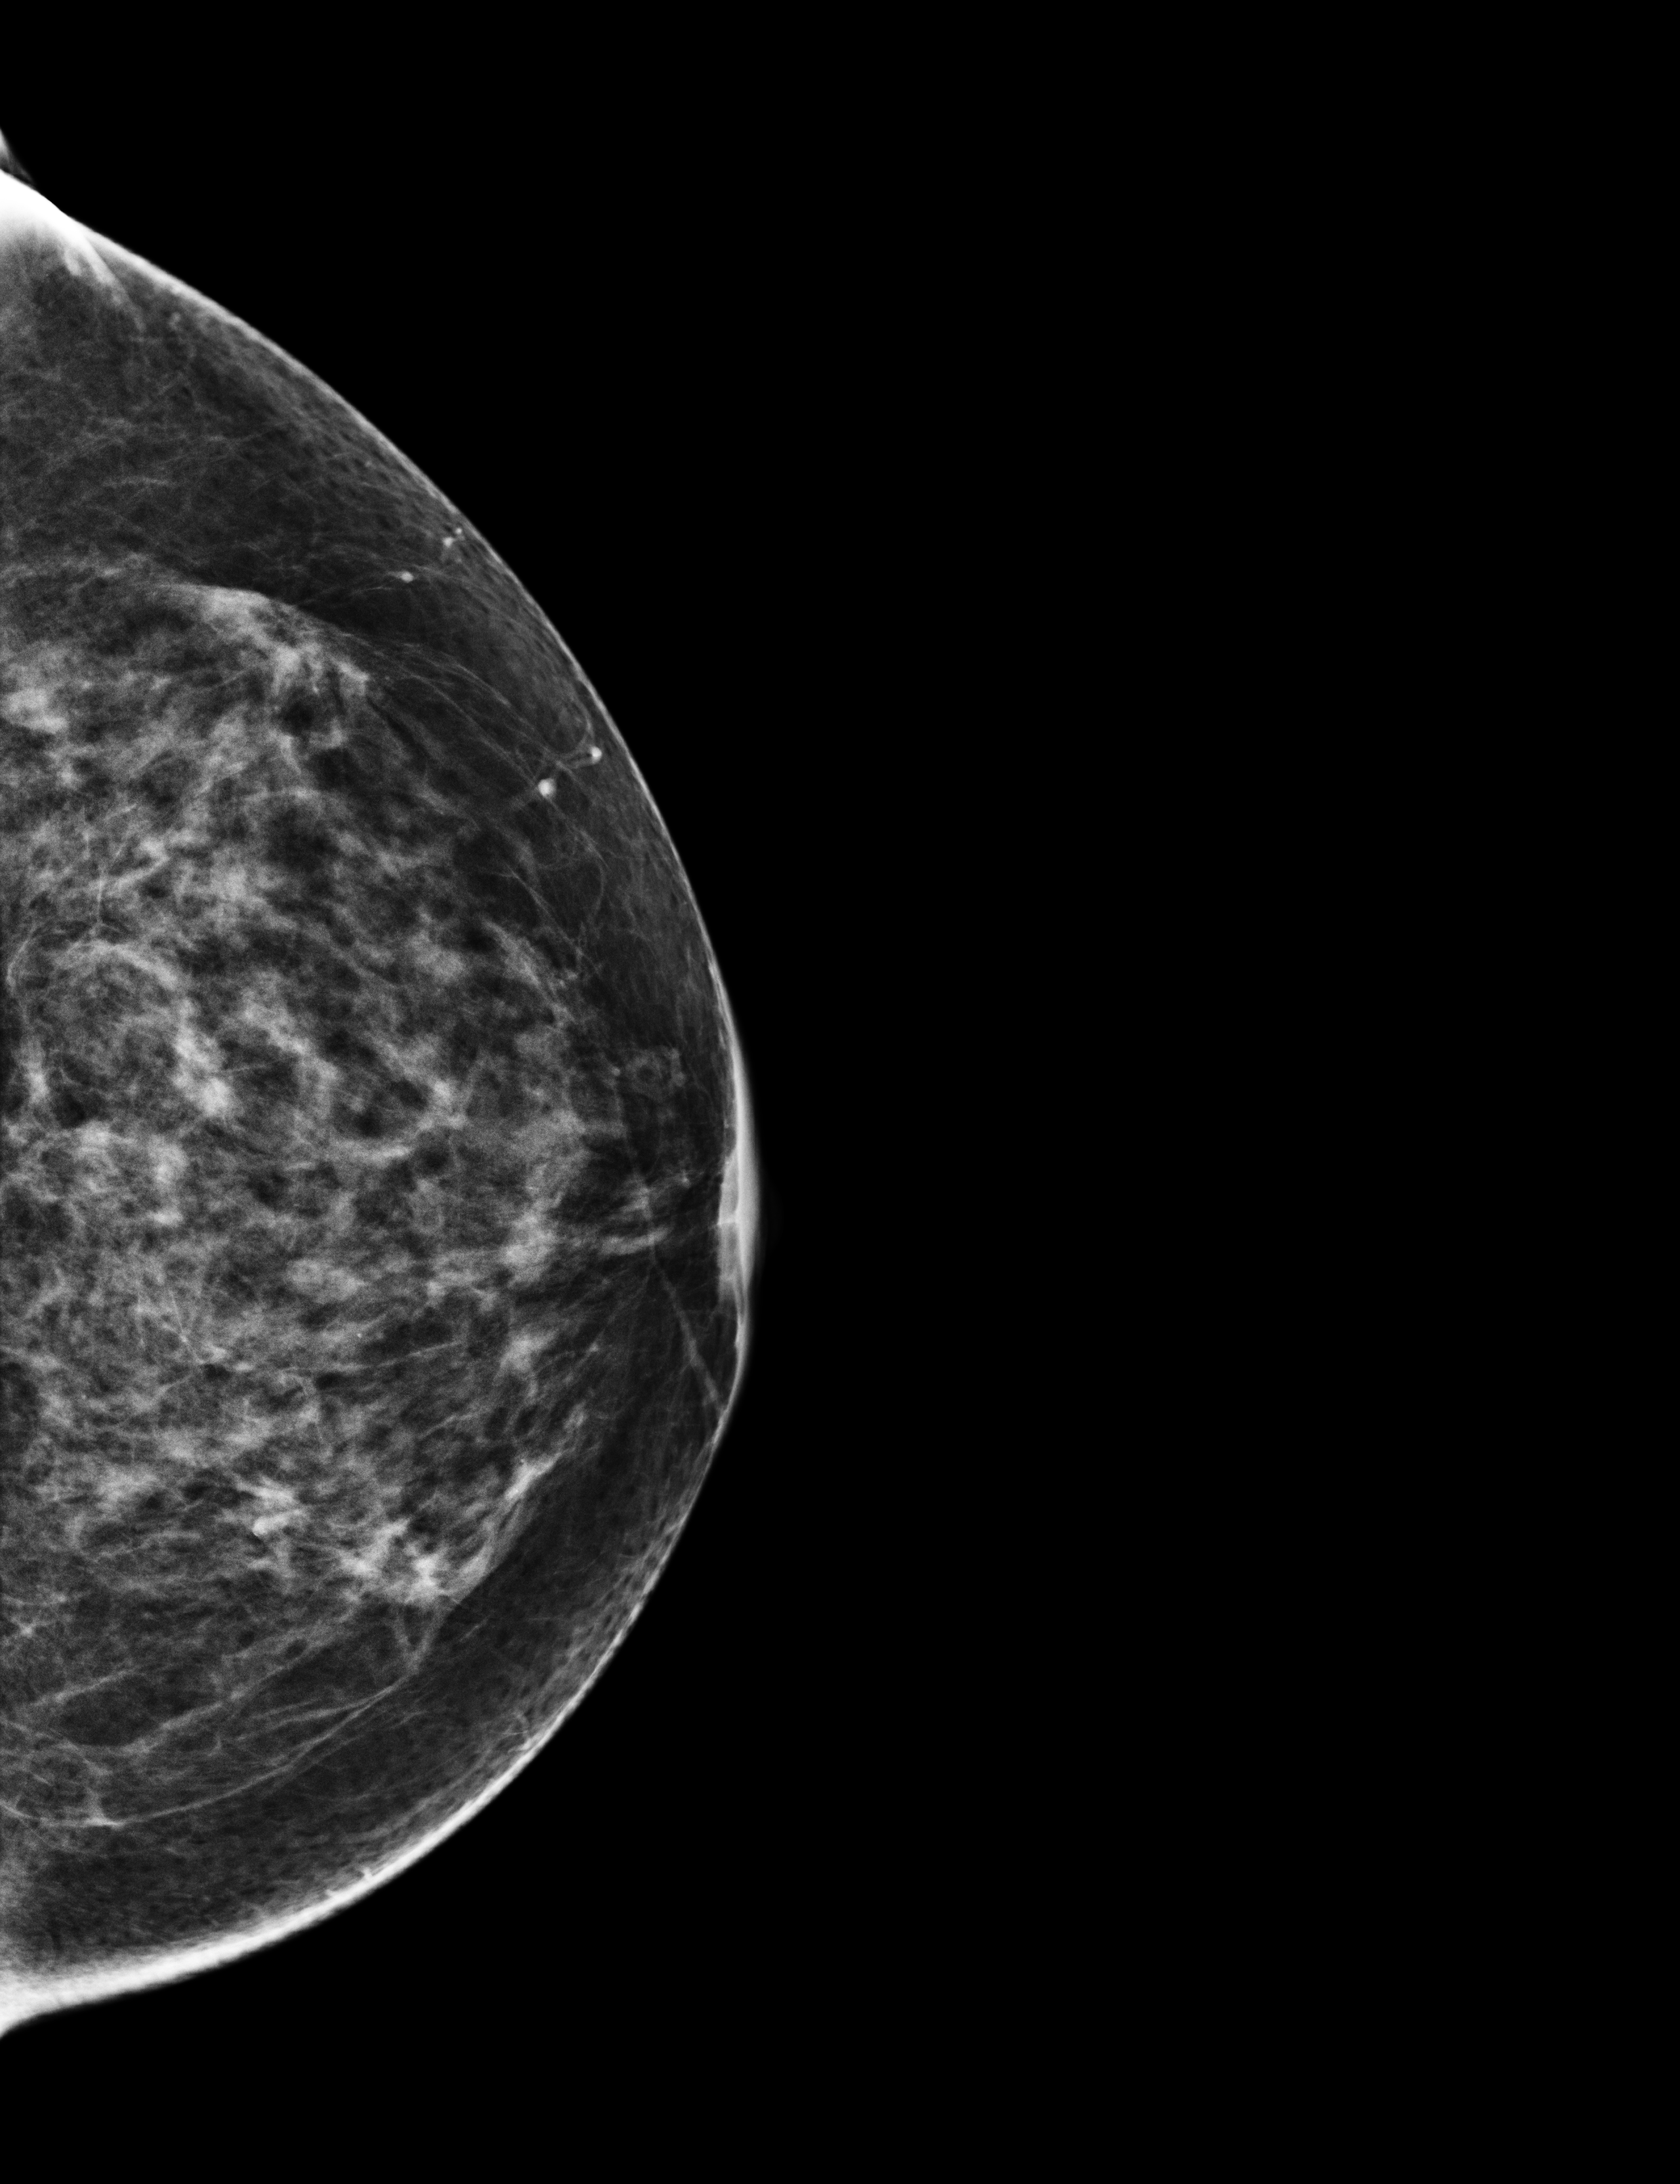
Full-field digital mammogram (FFDM), left breast, craniocaudal (CC) view, screening examination. Female patient, age 70 years.
- breast density at the screening exam (both breasts): heterogeneously dense (BI-RADS density category c)
- final BI-RADS category for the screening round (tomosynthesis exam, both breasts): category 2
- recall: no recall after this screen